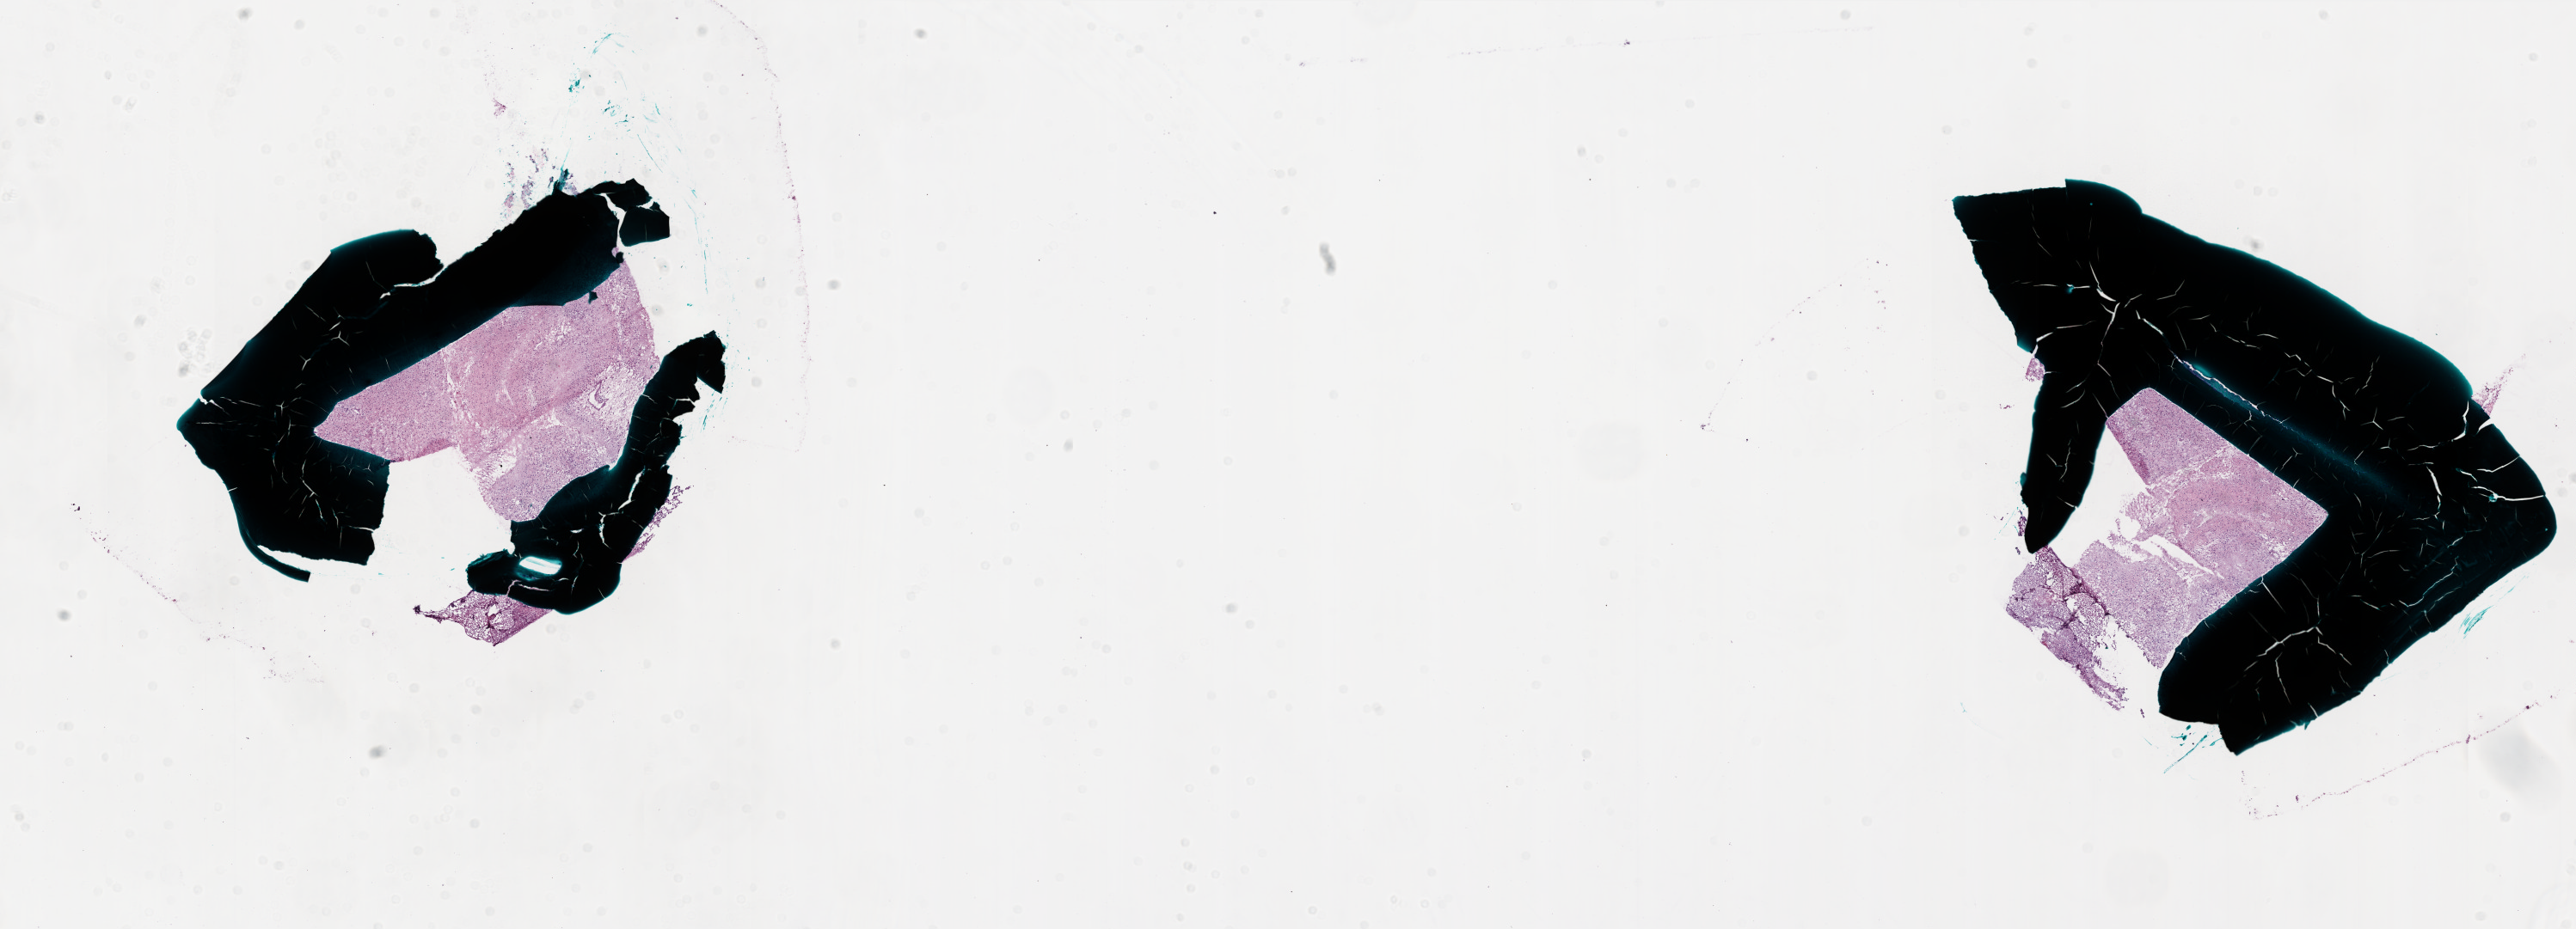
H&E-stained whole-slide image, a low-resolution overview of the entire scanned area, about 24.0 x 8.7 mm, frozen section from the bottom of the tissue portion, sample: primary tumour, brain. Male, age 67 years at initial diagnosis.
Pathologic diagnosis: Glioblastoma.